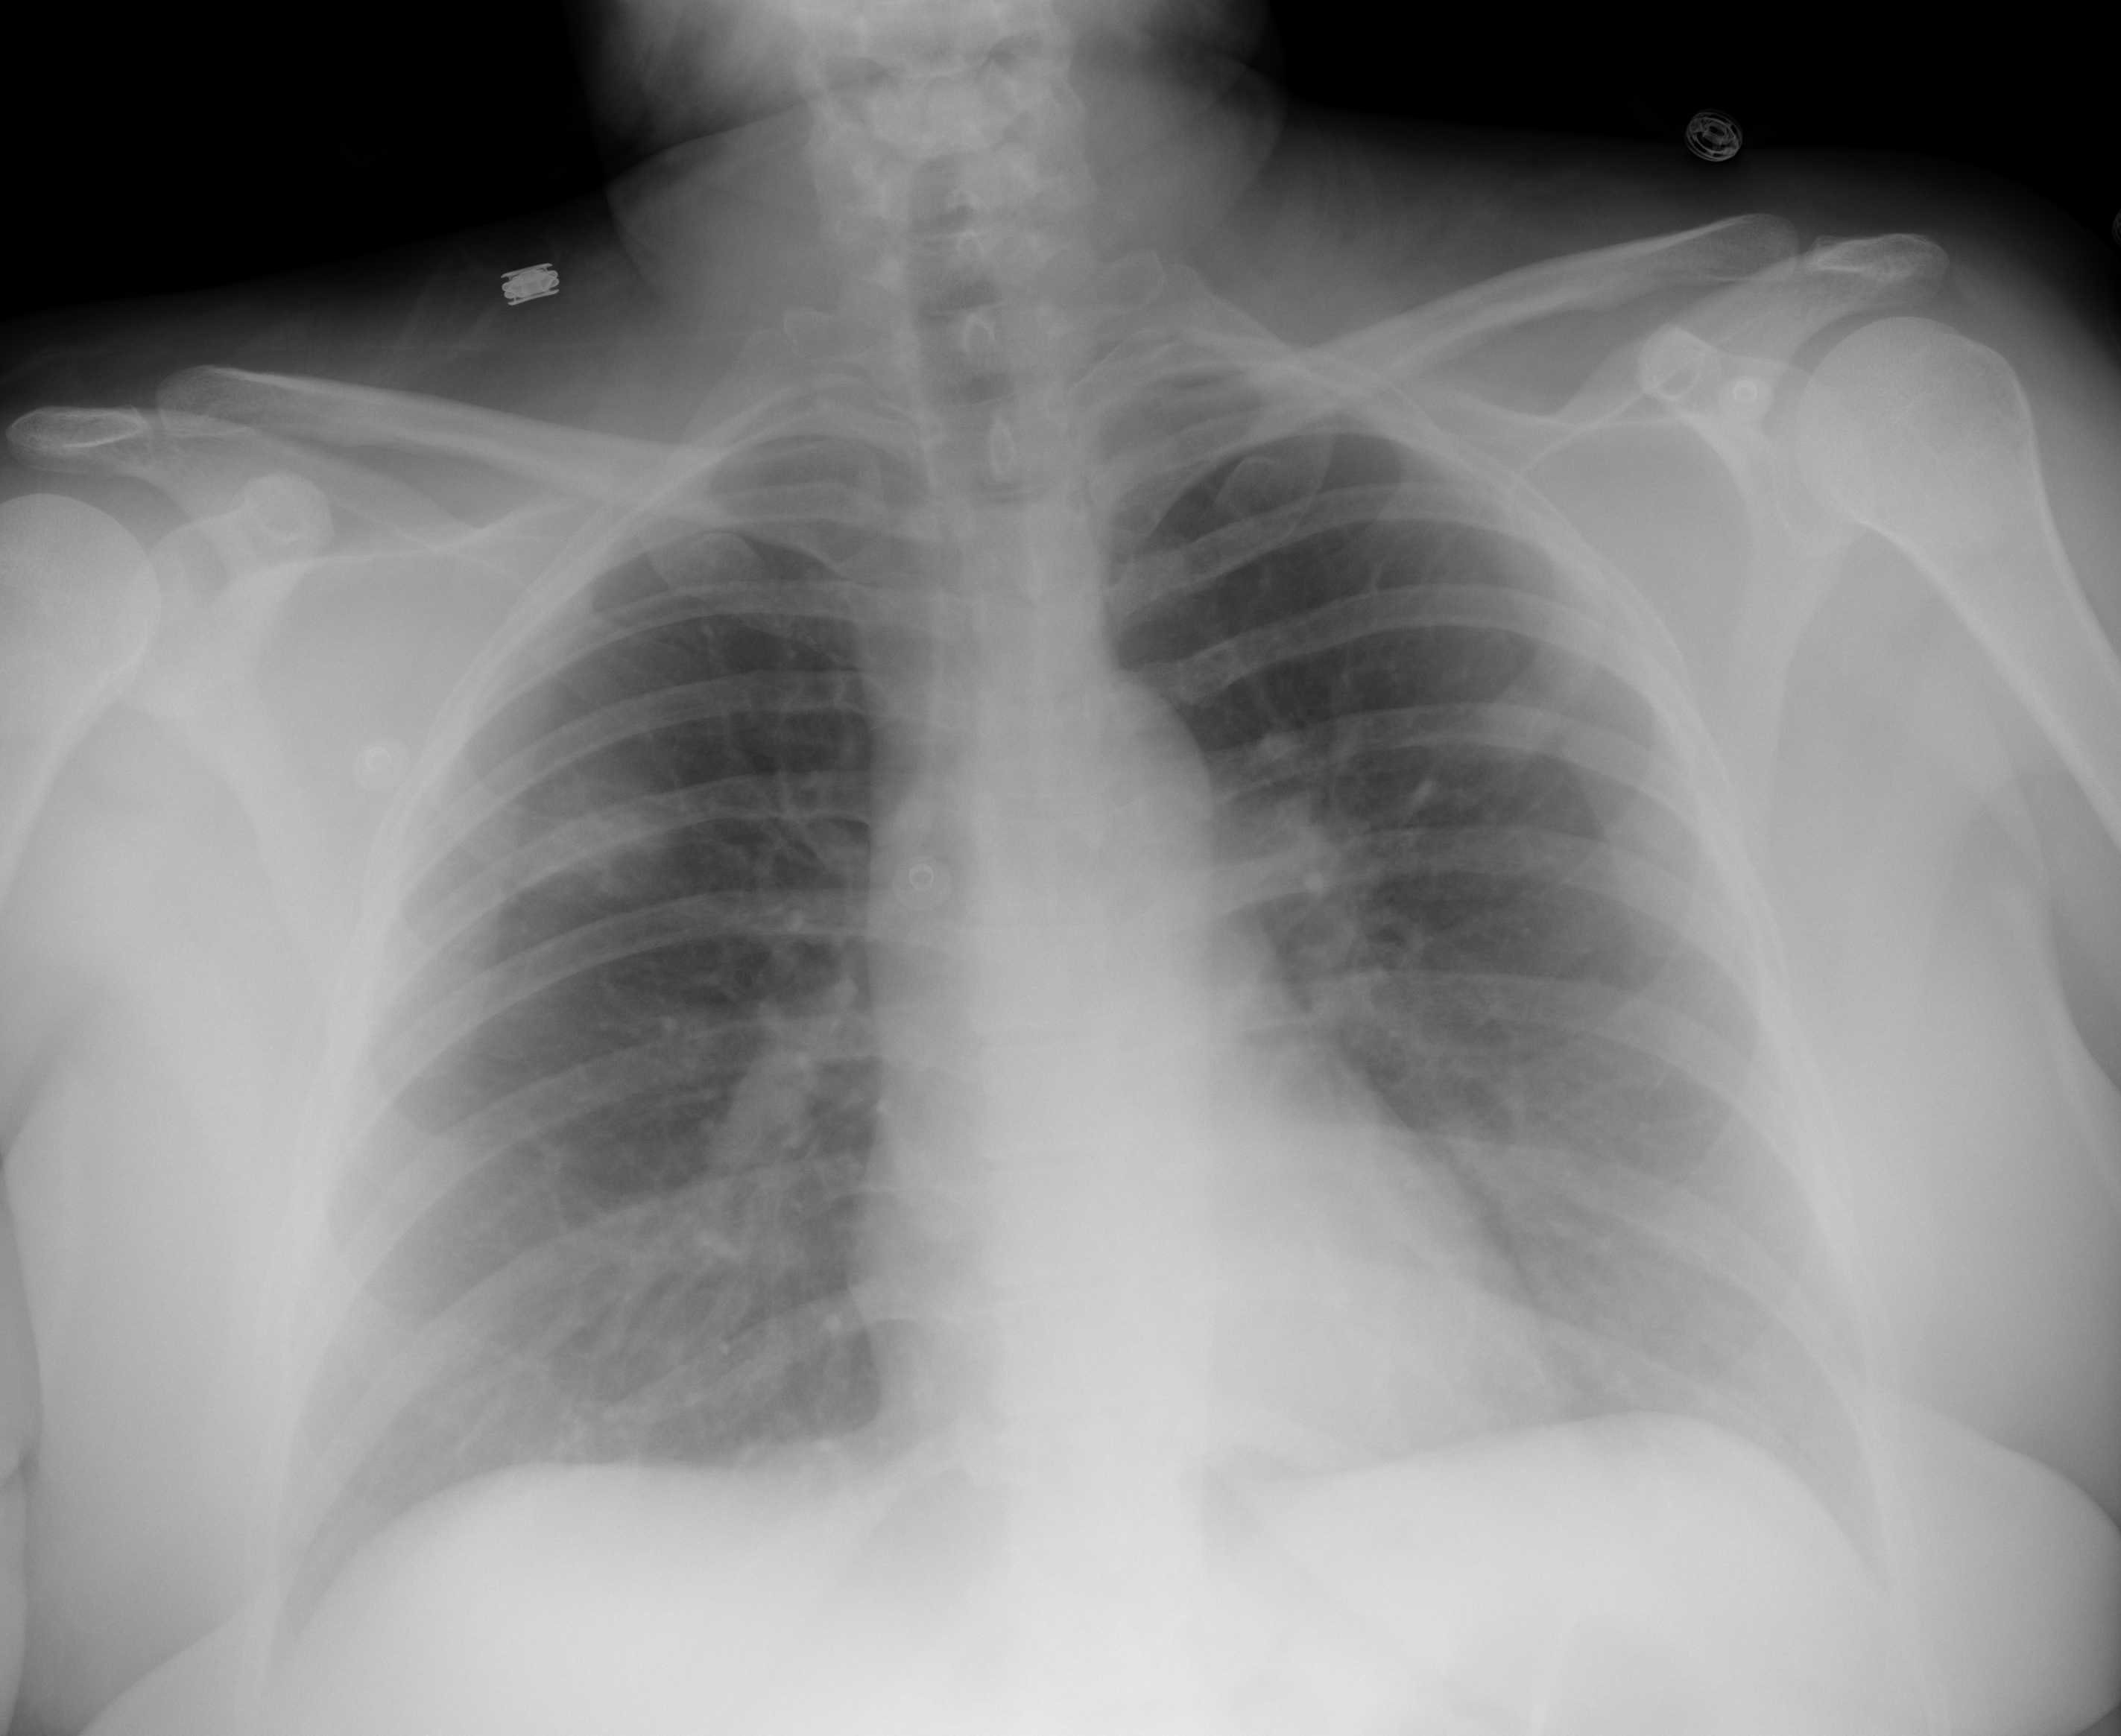
Chest X-ray (portable), AP projection. Female patient, age 40 years; imaged 6 days after the COVID-19 diagnosis.
Key findings recorded by the radiologist: Subtle airspace opacity in the right upper lobe.